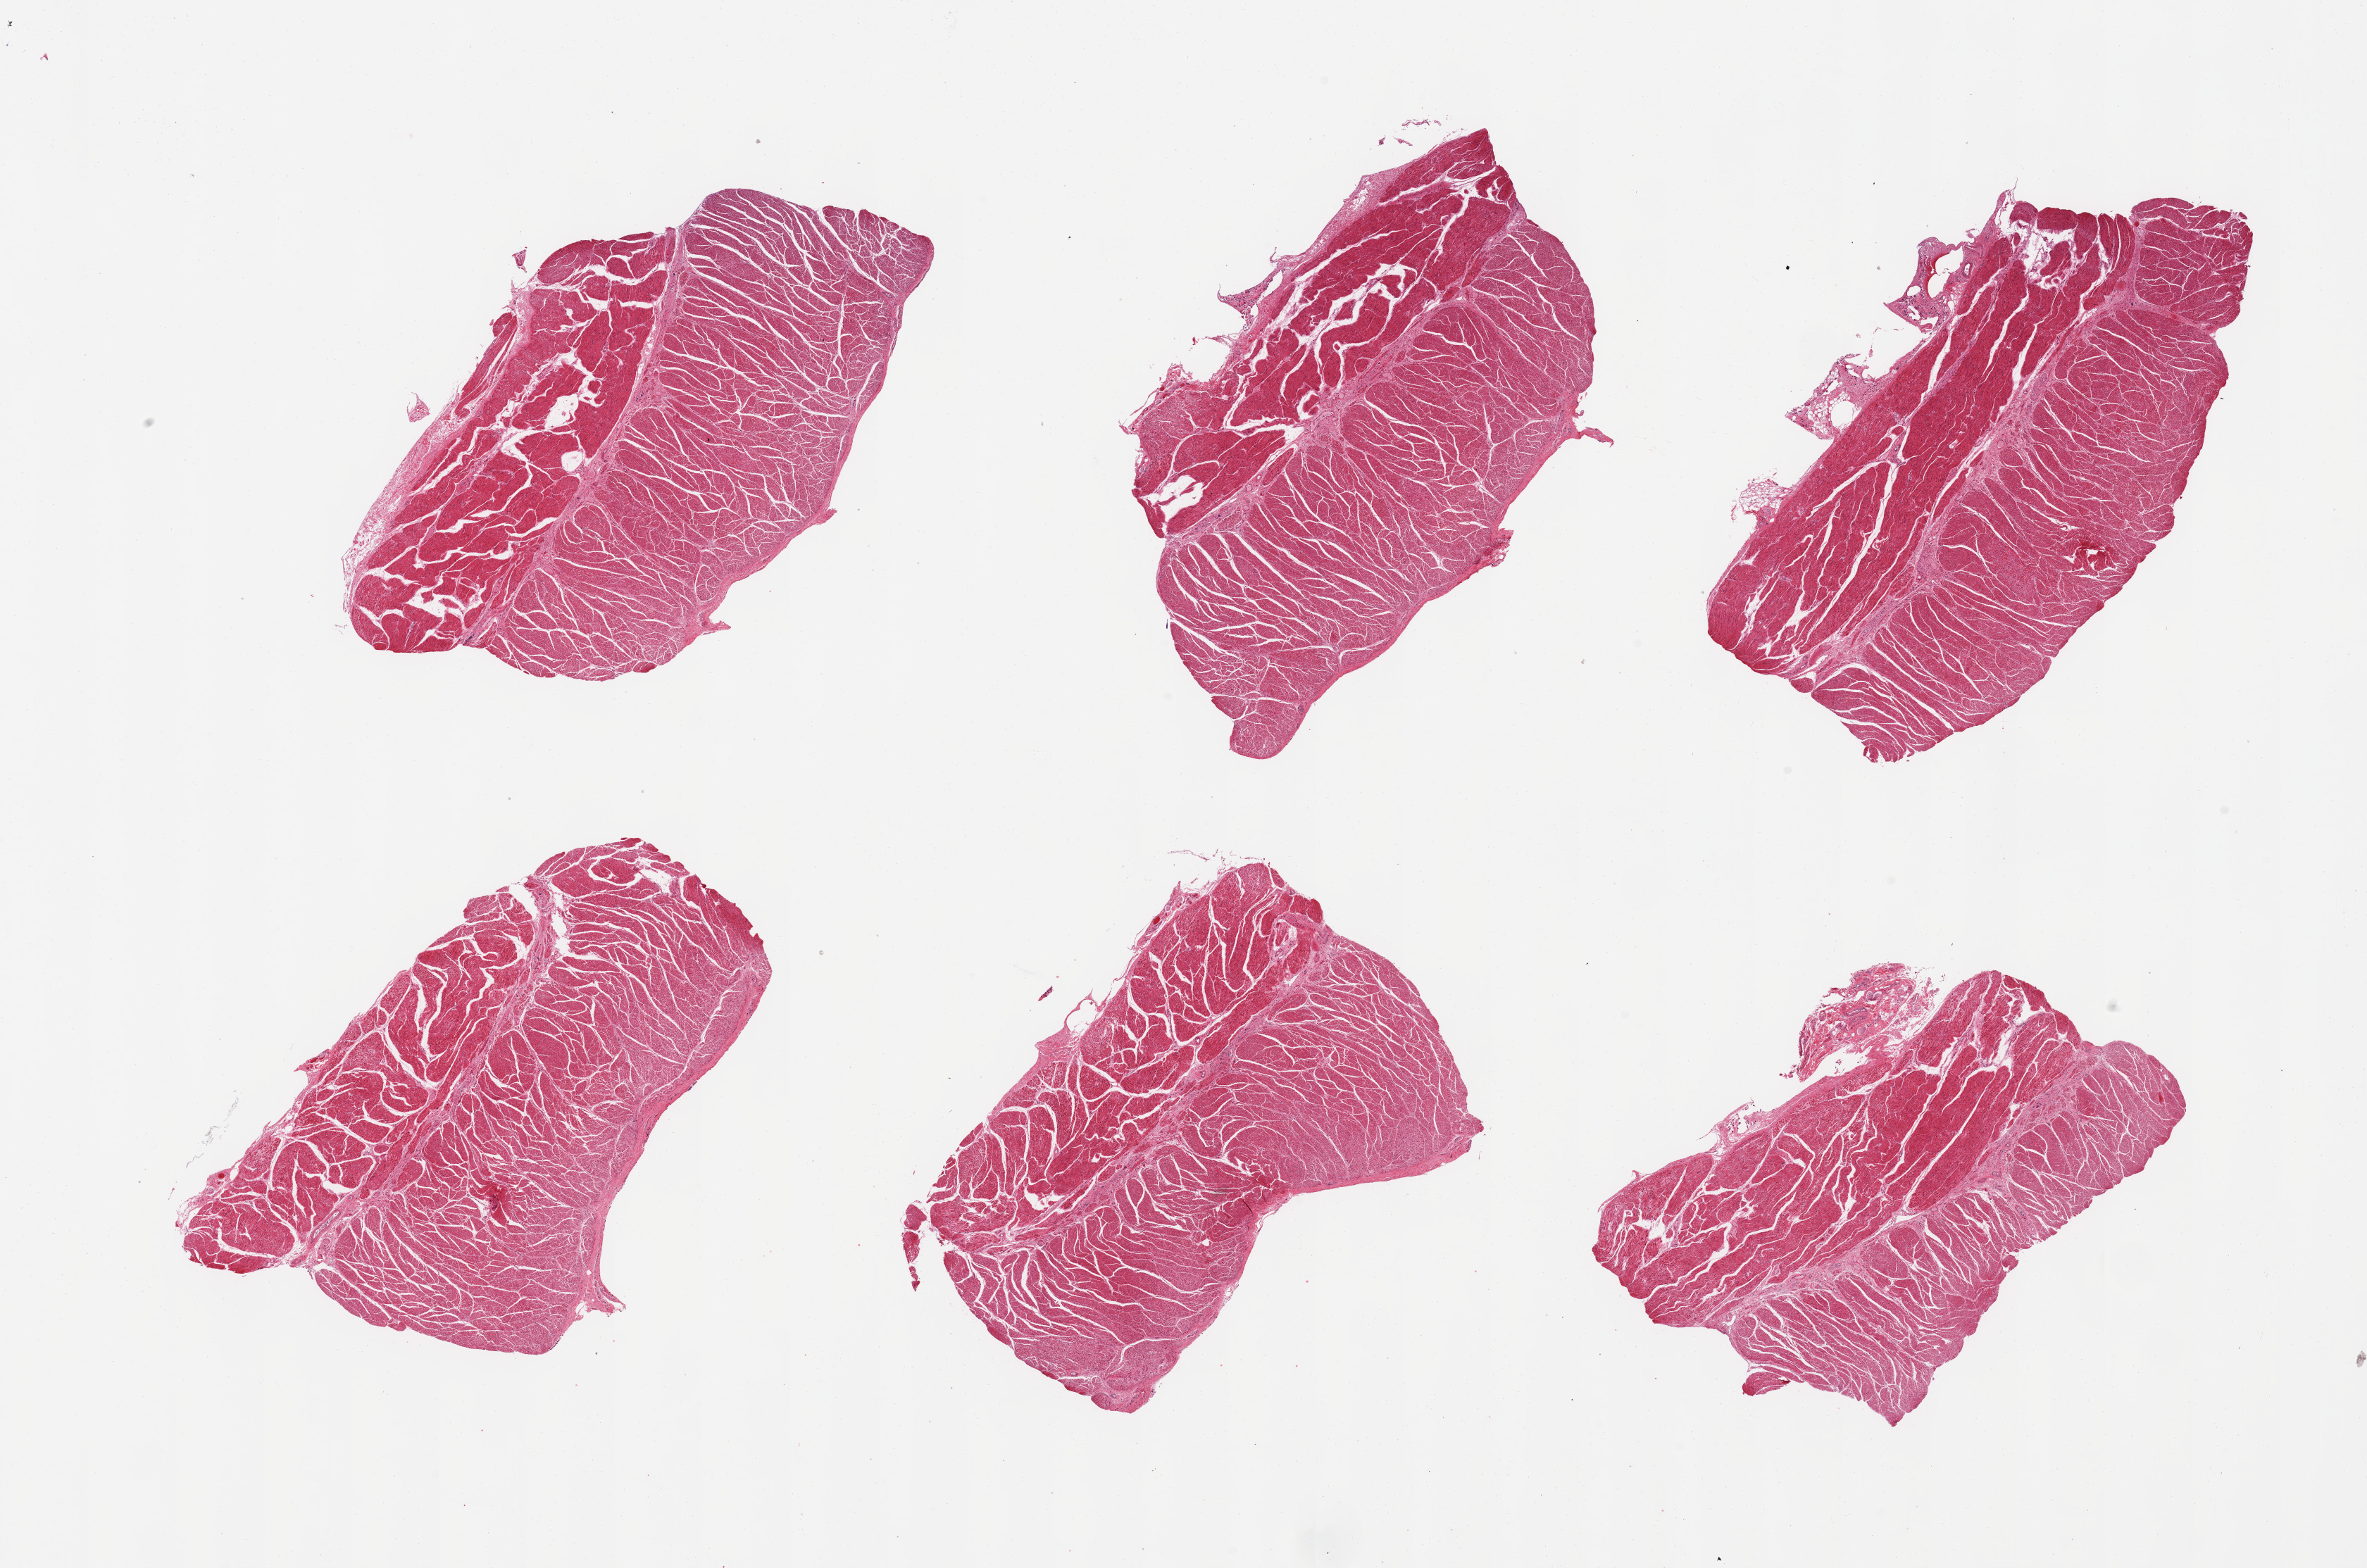
Whole-slide image, haematoxylin and eosin stain, brightfield, shown as a low-resolution overview of the whole scanned area (about 26.6 x 17.6 mm, acquisition: 20x scan). PAXgene-fixed paraffin-embedded (PFPE) section. Sampled site (target tissue): gastroesophageal junction. Donor tissue sample. Male donor.
Reviewer comment on this tissue sample: 6 pieces; minute foci of squamous epithelial cells in submucosal stroma; otherwise well trimmed muscle.